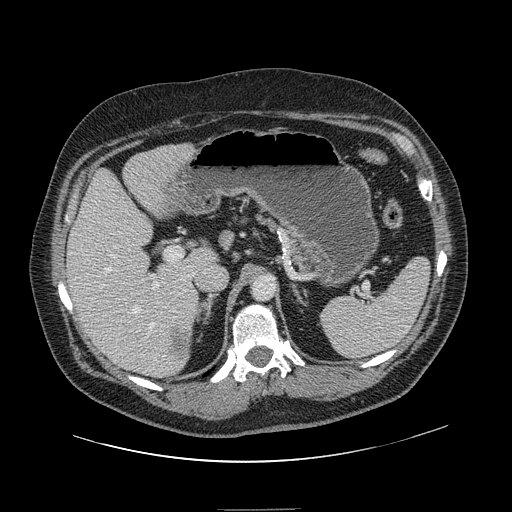
Contrast-enhanced abdominal CT, one axial slice. Slice 87 of 154 in the series (ordered by position). 120 kVp. Intravenous contrast given. Soft-tissue window (W 400 / L 40 HU). 2.5 mm slice thickness. 512 × 512 image matrix. Male patient, age 61 years. Case-level facts recorded for this patient, not image findings: diagnosis: colorectal cancer liver metastases, imaged before liver resection; multiple liver metastases: yes; largest metastasis: 2.6 cm; disease in both lobes: yes.
Structures marked on this image (outlined manually by an expert reader):
- hepatic veins: bounding box [x1, y1, x2, y2] px = [105, 246, 157, 361]
- liver: [68, 144, 215, 377]
- planned liver remnant (the part of the liver to remain after resection): [68, 148, 215, 366]
- portal vein (with intrahepatic branches): [100, 254, 159, 289]
- liver metastasis: [171, 330, 190, 361]